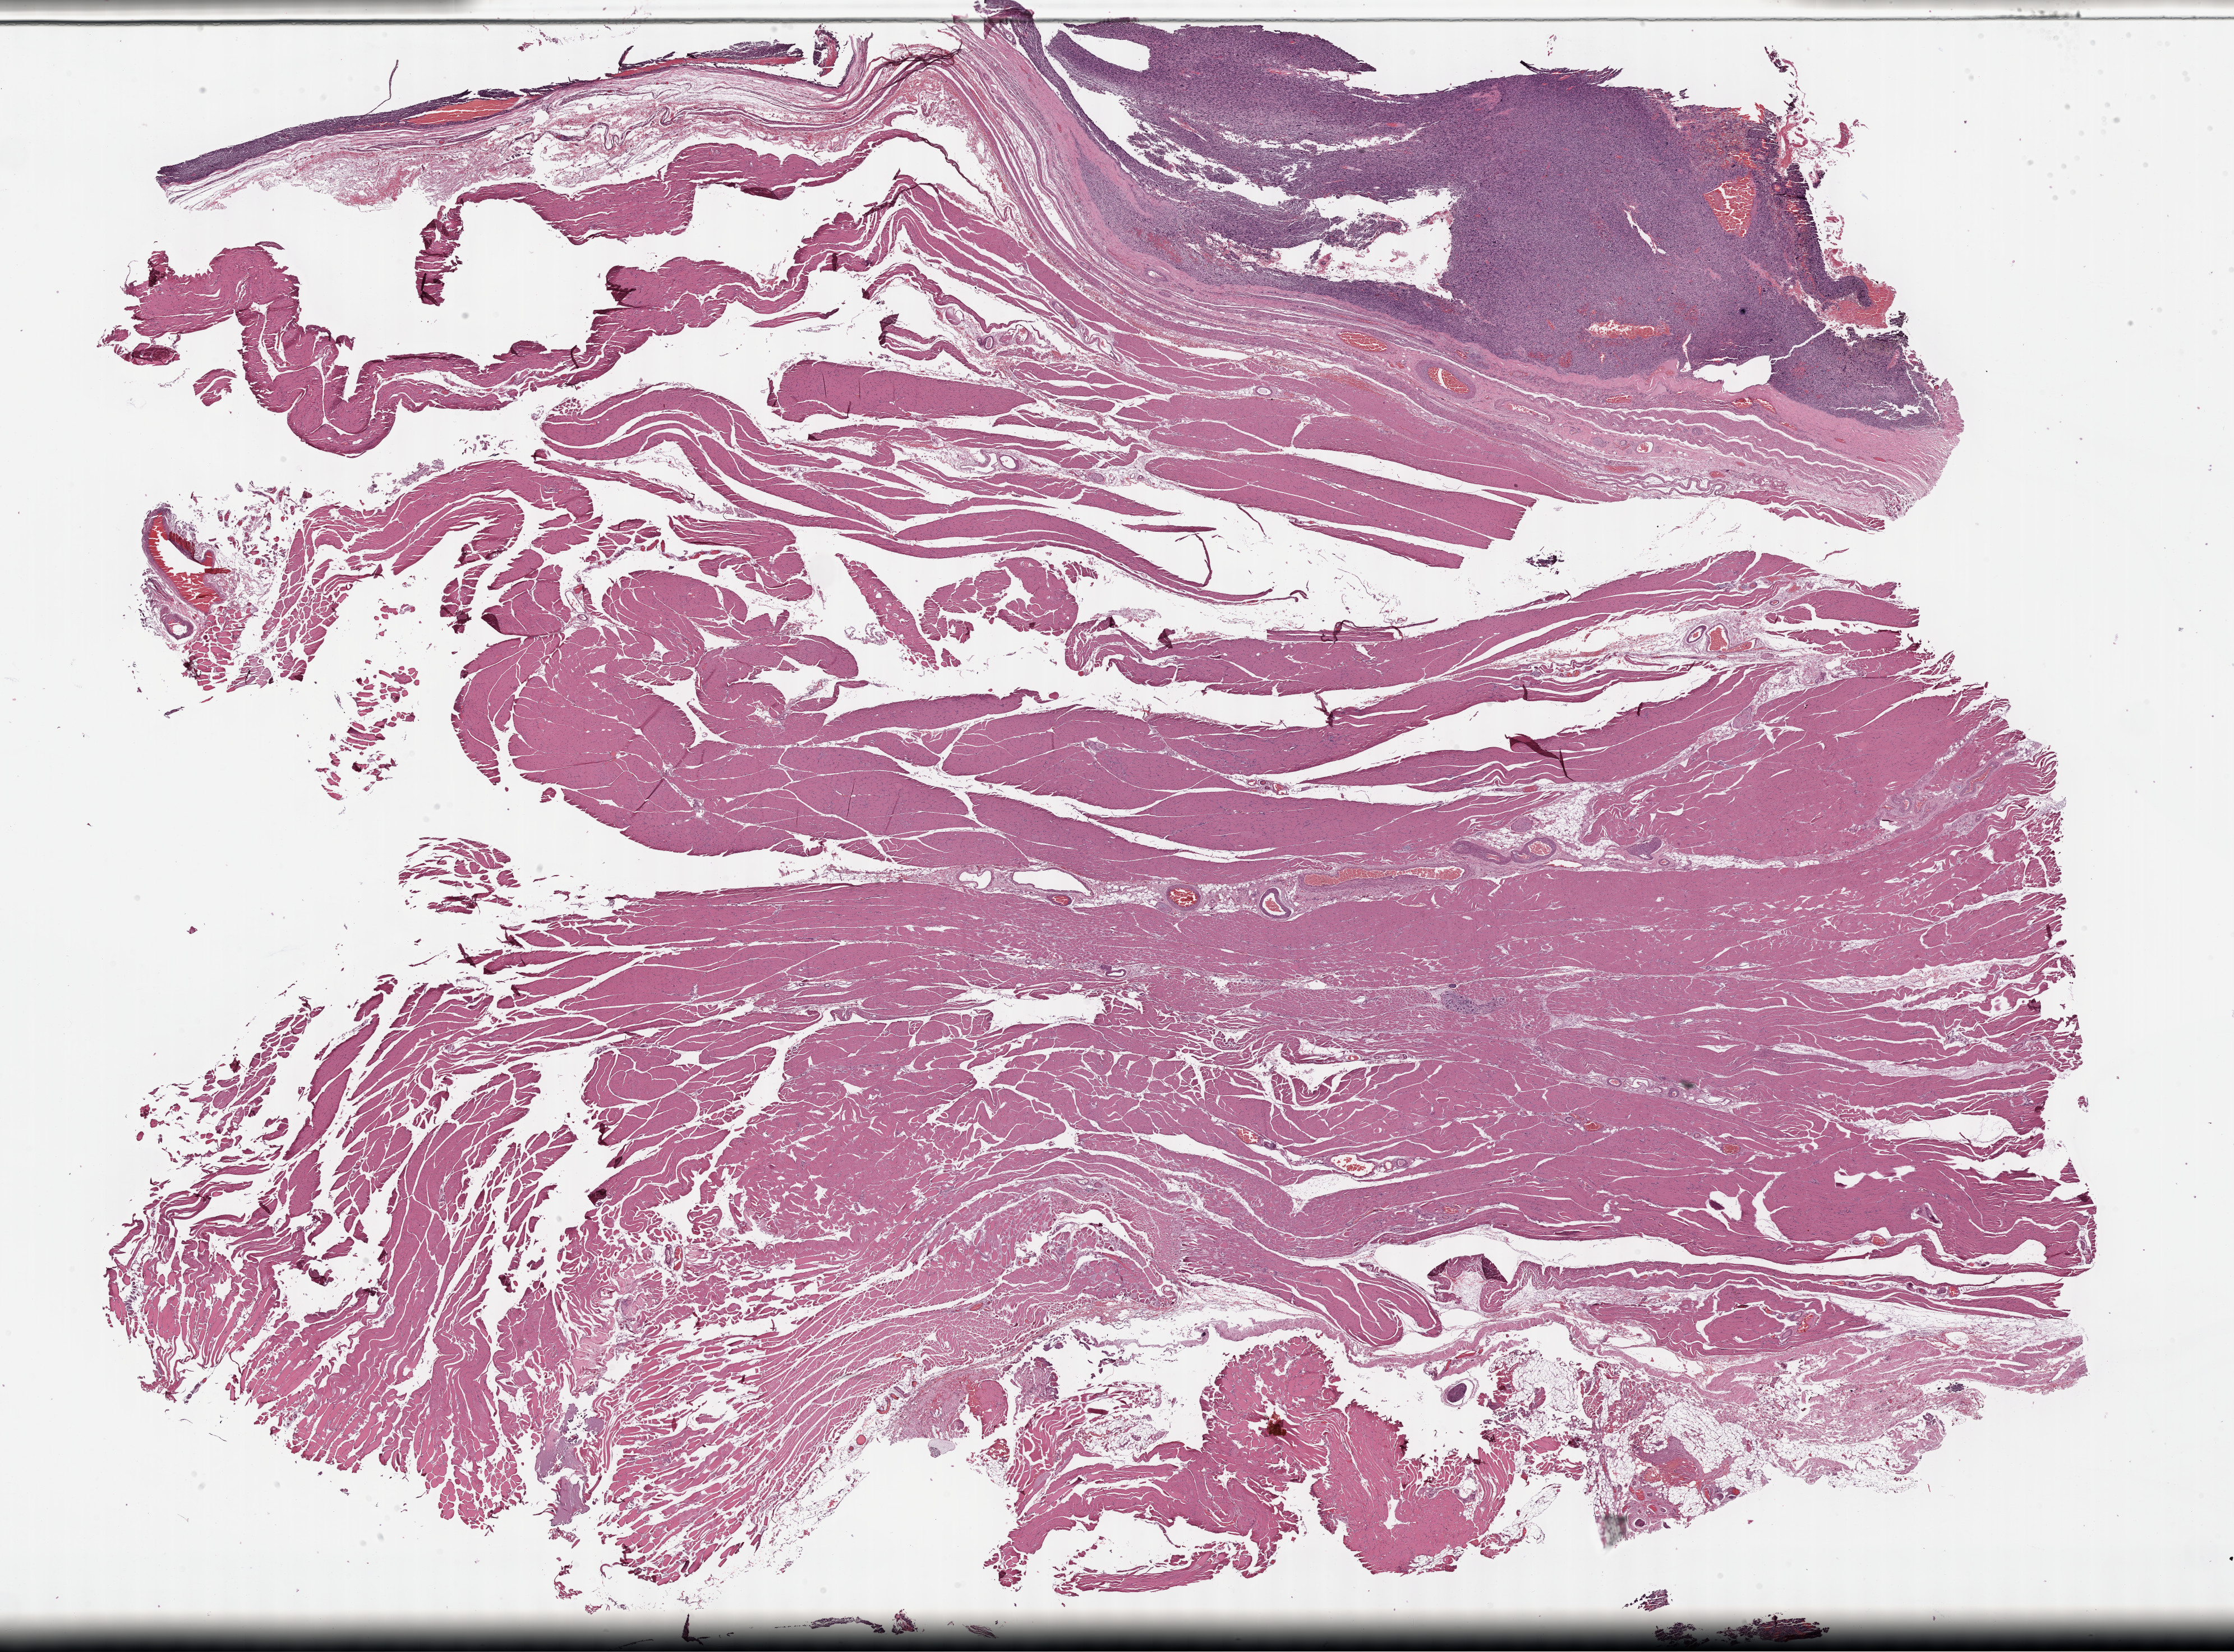
Whole-slide histology image, Hematoxylin and eosin (H&E) stained — a low-resolution overview of the entire scanned area, about 32.2 x 23.8 mm (from a 40x scan), FFPE section, connective, subcutaneous and other soft tissues, primary tumour sample. Patient: female, age at initial diagnosis 80 years.
Histologic diagnosis: Undifferentiated sarcoma (connective, subcutaneous and other soft tissues of lower limb and hip).